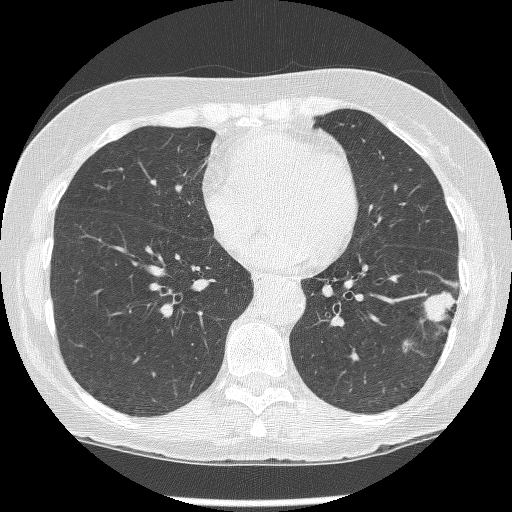
Axial slice from a low-dose chest CT screening exam. First (baseline) screen. Lung window (W 1500 / L -600 HU). 1.25 mm slice thickness. Lung (sharp) reconstruction kernel (BONE). Slice 98 of 247 in the series. Female, age 62 years at enrolment.
• Expert-annotated lung lesion, bounding box (x1, y1, x2, y2) in pixels: (415, 283, 460, 341).
• The screening reader recorded 2 non-calcified nodules or masses ≥4 mm on this exam; which of them this box marks is not recorded.
• Official screen result: positive, change unspecified: nodule(s) >= 4 mm or enlarging nodule(s), mass(es), or other non-specific abnormalities suspicious for lung cancer.
• Participant outcome: lung cancer diagnosed 15 days after this screen — non-small cell carcinoma, left lower lobe, stage IIIB (AJCC 6th edition), 23 mm at pathology.